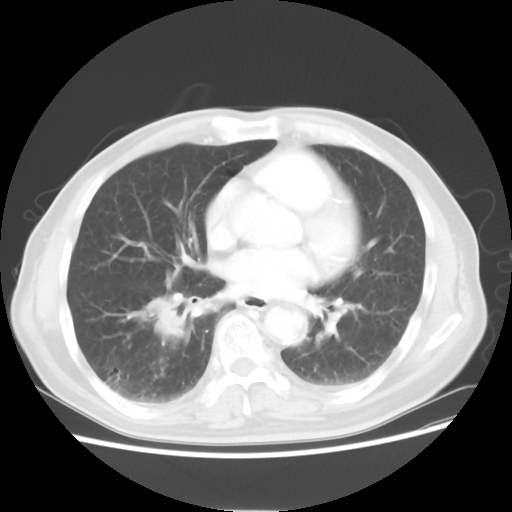
Chest CT, one axial slice; position 28 of 58 along the scan axis; lung window (W 1500 / L -600 HU); 5 mm slice thickness; 512 × 512 image matrix, field of view 360 × 360 mm. Patient: male, 74 years. From the clinical record (not read from this slice): clinical TNM (as recorded): T1c N1 M1.
Outlined on this slice (rectangle marked by the reading radiologist):
- lung tumour (recorded histology: adenocarcinoma): bounding box [x1, y1, x2, y2] px = [127, 292, 194, 354]